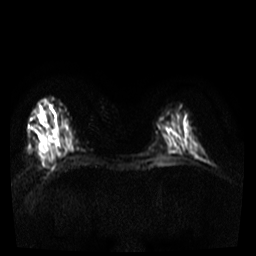
Breast MRI, one axial slice; diffusion-weighted series; image 2 of 4 stored at this slice position (different b-values; order by instance number); 3 T; 5 mm slice thickness; 256 × 256 image matrix, field of view 300 × 300 mm. Female patient.
Annotated regions visible in this slice (manually delineated by an expert):
- tumour on diffusion-weighted imaging: box from (x=40, y=111) to (x=49, y=151) px